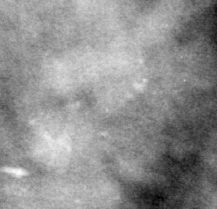
Region of interest cut from a scanned film mammogram (one marked finding); left breast; MLO view; BI-RADS breast density category 3 (scale 1–4).
Calcifications, morphology pleomorphic, distribution clustered; BI-RADS assessment category 3; pathology result (as recorded, not read from the image): malignant.